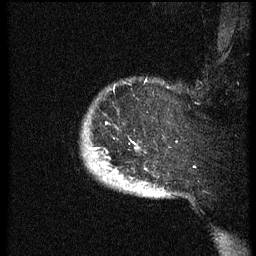
Breast MRI (dynamic contrast-enhanced), one sagittal slice; slice 54 of 60 in the series (ordered by position); dynamic contrast-enhanced series, image 2 of 3 at this slice position (ordered by acquisition); 1.5 T; TE 4.2 ms, TR 8.4 ms; 256 × 256 image matrix, field of view 200 × 200 mm. Patient: female, 38 years. From the clinical record (not read from this slice): setting: breast cancer imaged before/during neoadjuvant chemotherapy; receptor status: HER2-positive.
Annotated regions visible in this slice (semi-automatic segmentation, software-assisted and operator-edited):
- analysis volume of interest (the breast-tissue region the enhancement analysis was run in; not a lesion): box from (x=84, y=81) to (x=171, y=198) px
- tumour enhancement mask (voxels above the 70 % enhancement threshold inside the analysis volume of interest): (x=104, y=158)–(x=124, y=179)